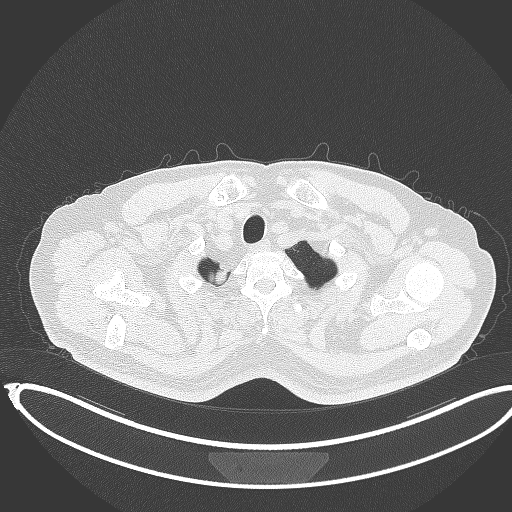
Chest CT, one axial slice; slice 346 of 403 in the series (ordered by position); reconstruction kernel B70f; 120 kVp; lung window (W 1500 / L -600 HU); 1 mm slice thickness; 512 × 512 image matrix. Patient: male, 68 years. From the clinical record (not read from this slice): clinical TNM (as recorded): T2a N0 M0.
Outlined on this slice (bounding box drawn by a radiologist):
- lung tumour (recorded histology: adenocarcinoma): bounding box (x1, y1, x2, y2) in pixels: (205, 262, 232, 290)